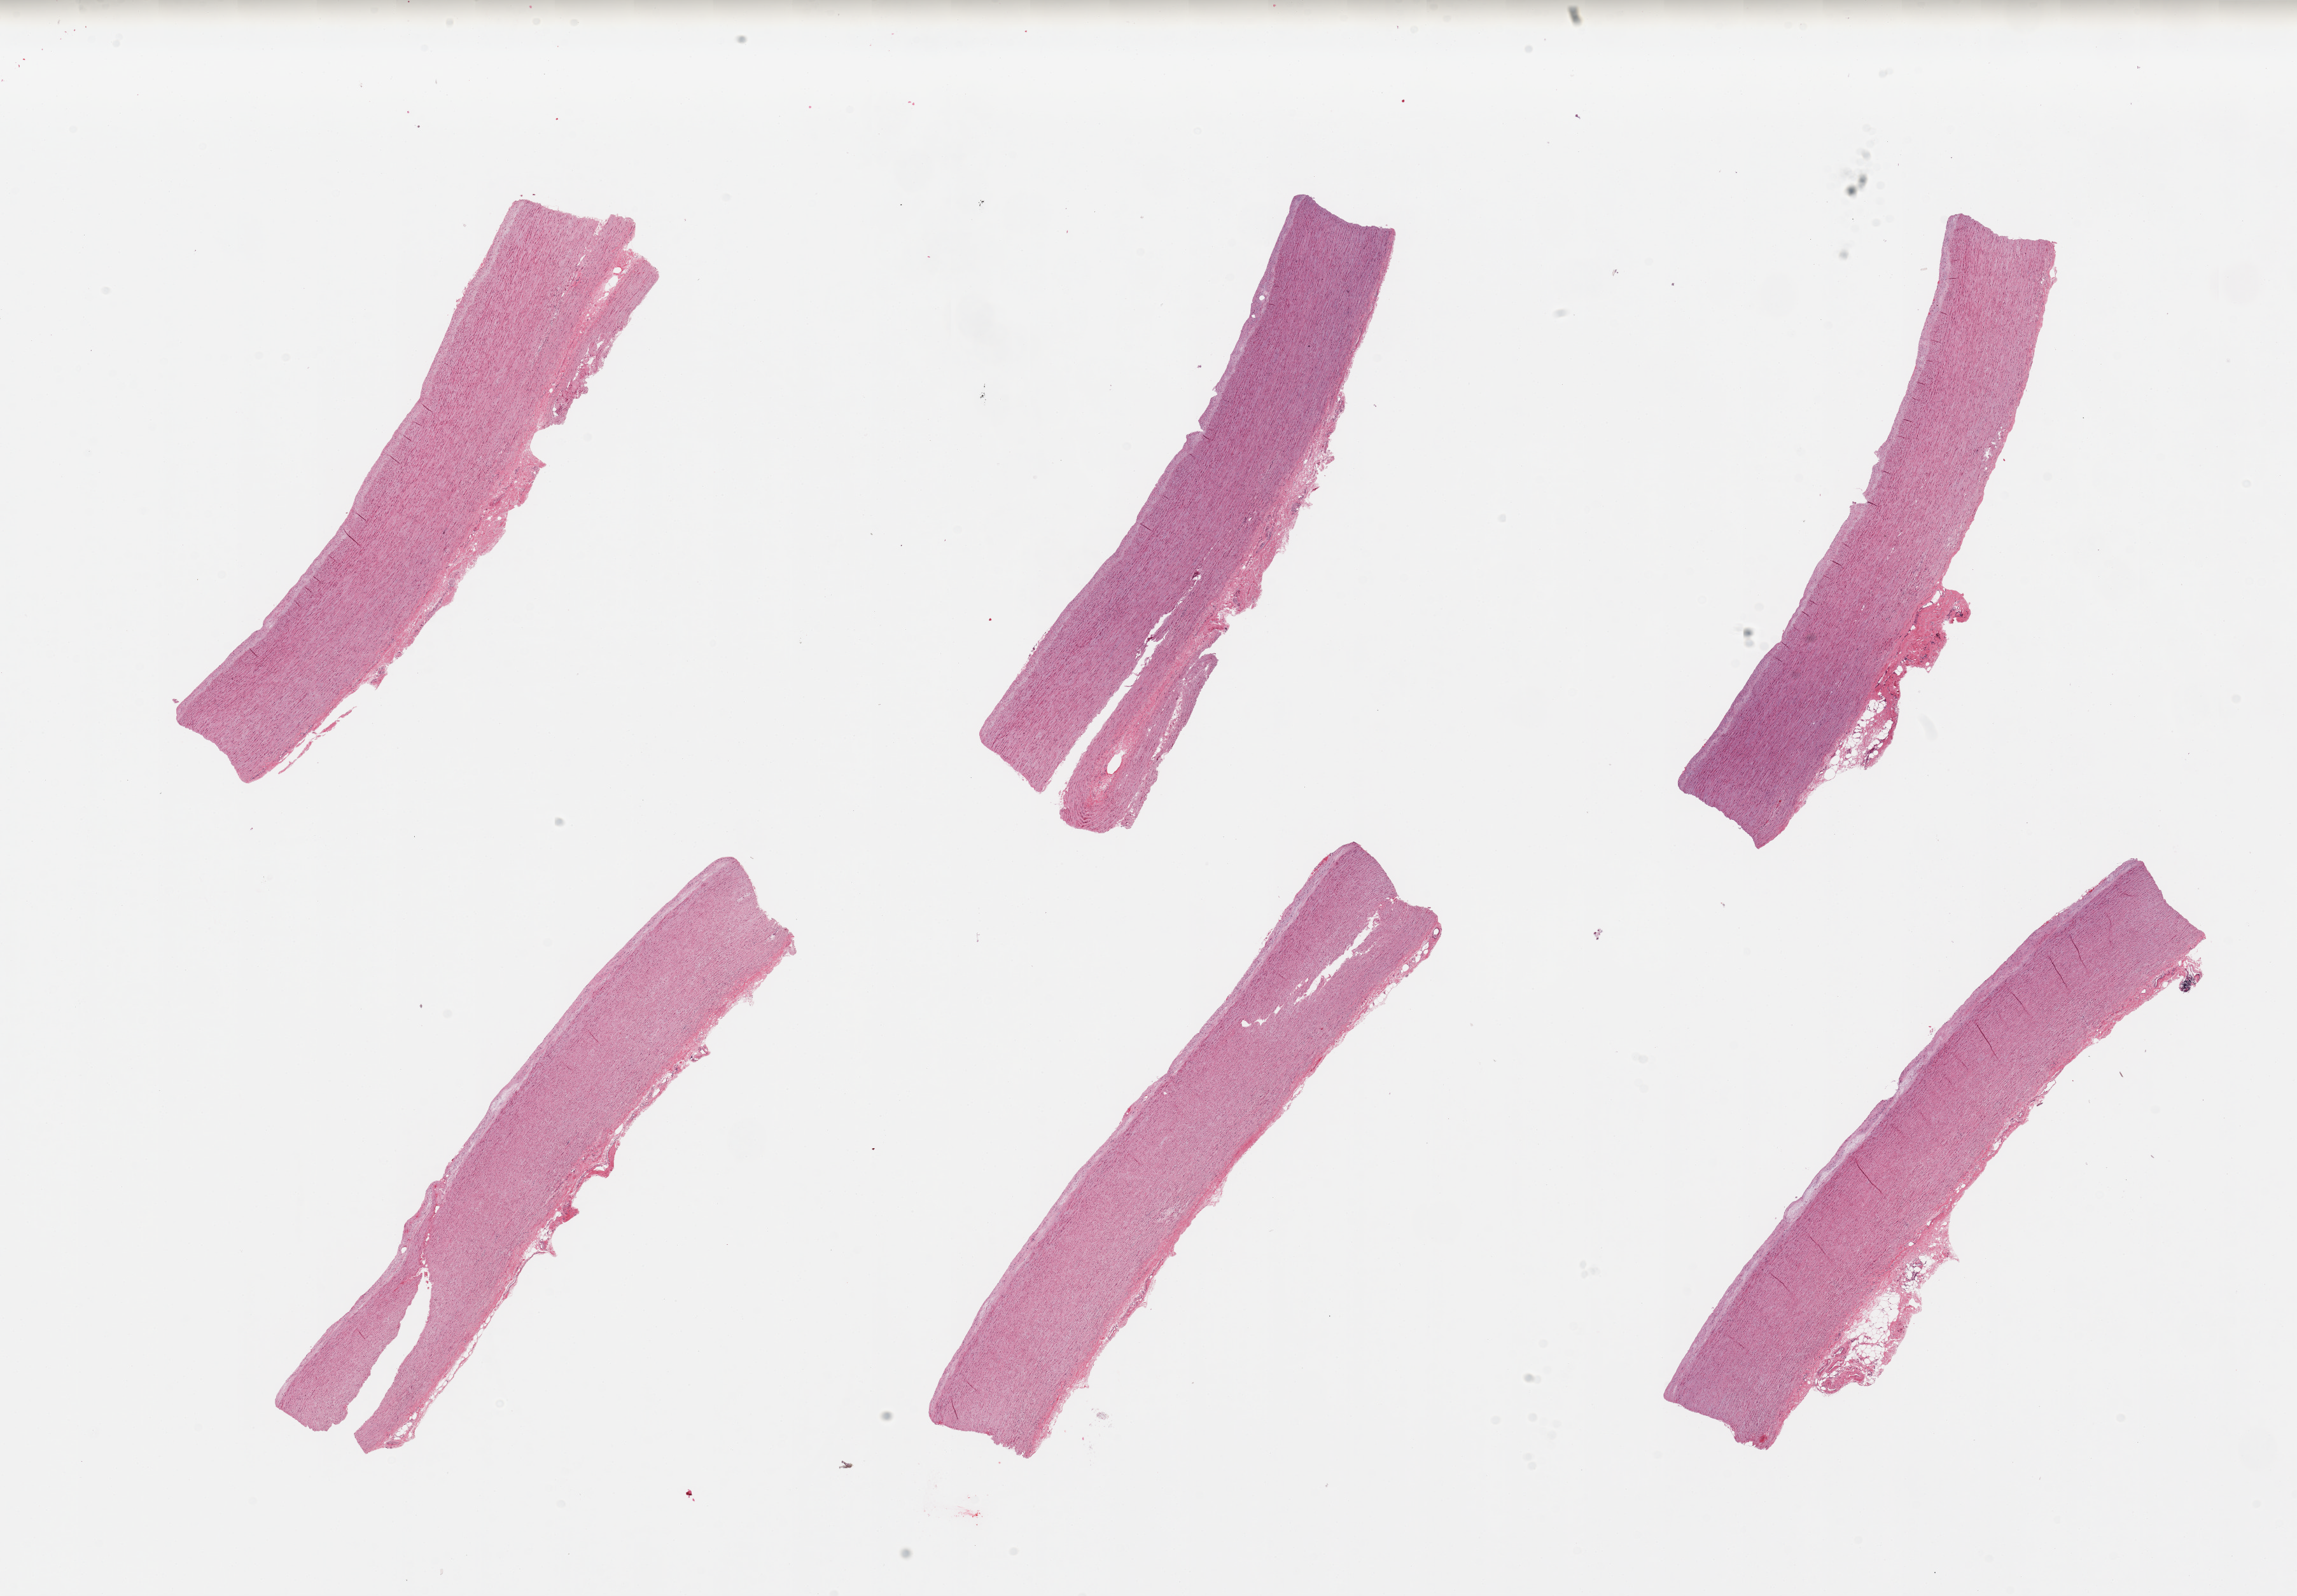
Haematoxylin and eosin whole-slide image — a low-resolution overview of the entire scanned area, about 28.5 x 19.8 mm (from a 20x scan), PAXgene-fixed paraffin-embedded (PFPE) section, section of aorta (target tissue), donor tissue sample. Donor sex: male.
Pathologist's review note for this sample: 6 pieces, 50--100microns atherotic deposition.